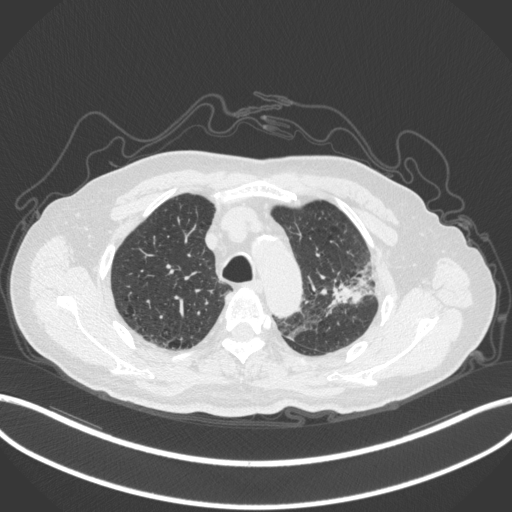
Chest CT, one axial slice; position 232 of 331 along the scan axis; lung window (W 1500 / L -600 HU); 512 × 512 image matrix, field of view 400 × 400 mm. Male patient, age 79 years. From the clinical record (not read from this slice): clinical TNM (as recorded): T2a N1 M1; histopathological grade: G3.
Structures marked on this image (rectangle marked by the reading radiologist):
- lung tumour (recorded histology: adenocarcinoma): bounding box (x1, y1, x2, y2) in pixels: (329, 256, 375, 307)